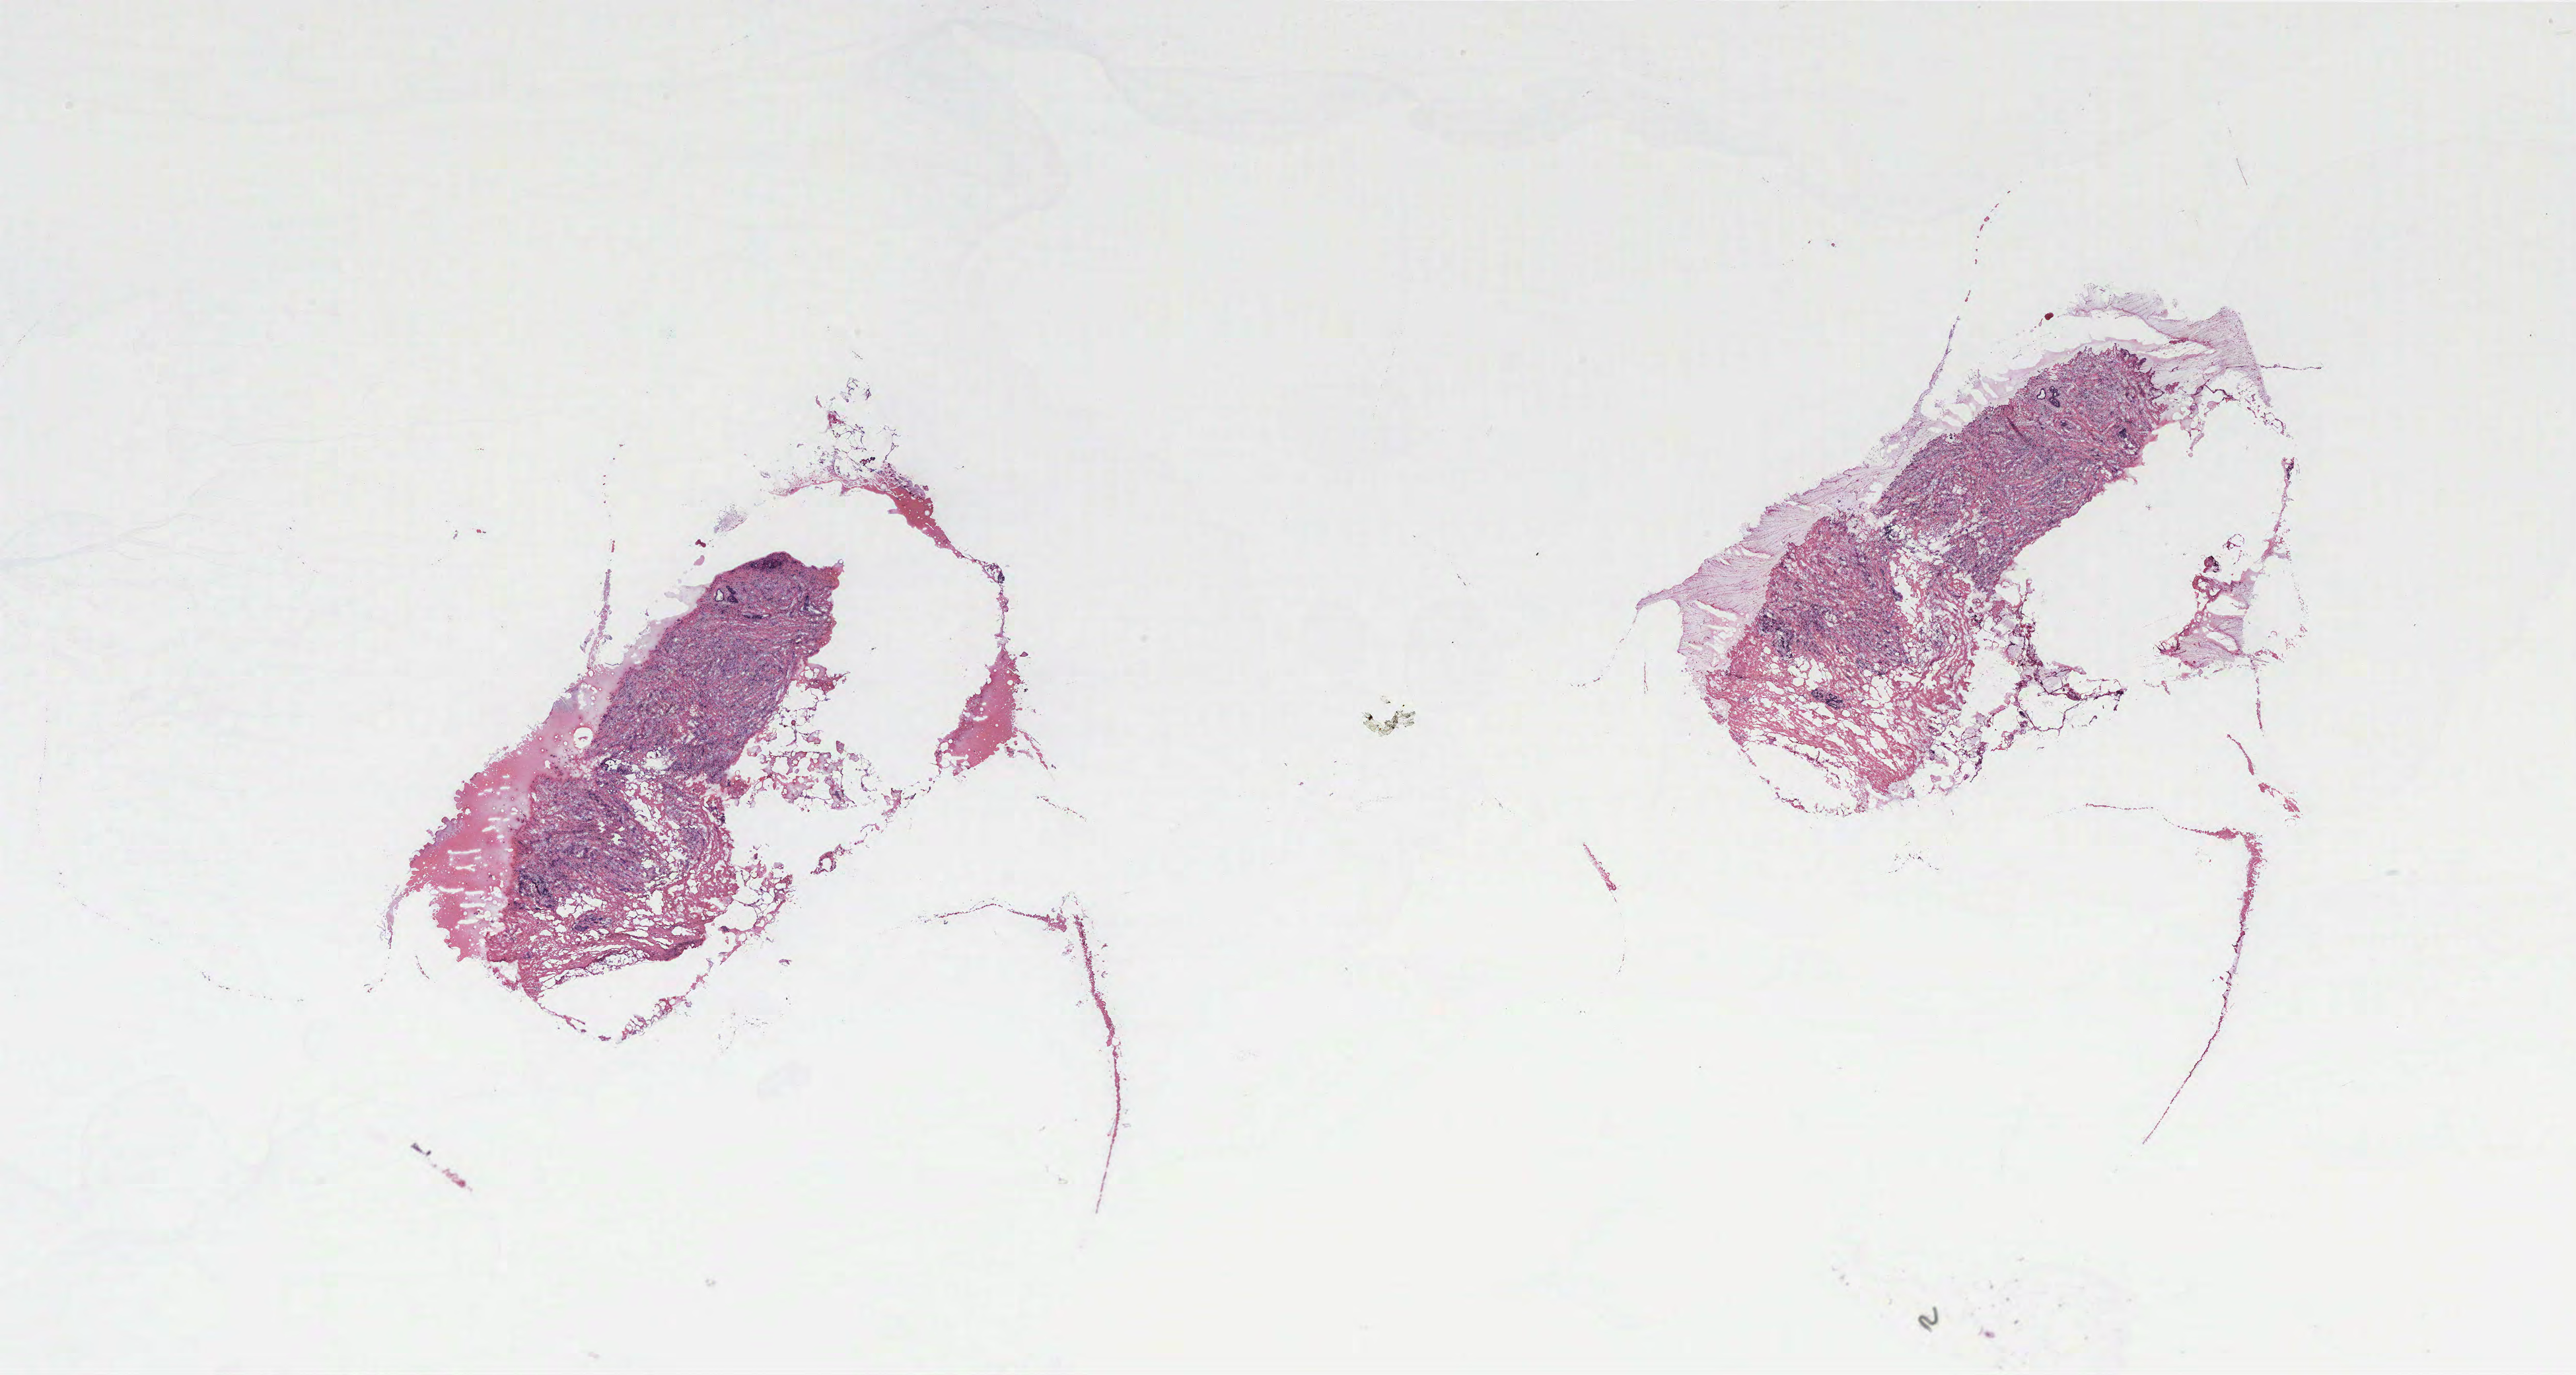
Whole-slide histology image, H&E — shown as a low-resolution overview of the whole scanned area (about 31.2 x 16.7 mm); breast, tissue type not recorded.
Patient diagnosis (cohort enrolment): breast cancer (breast).